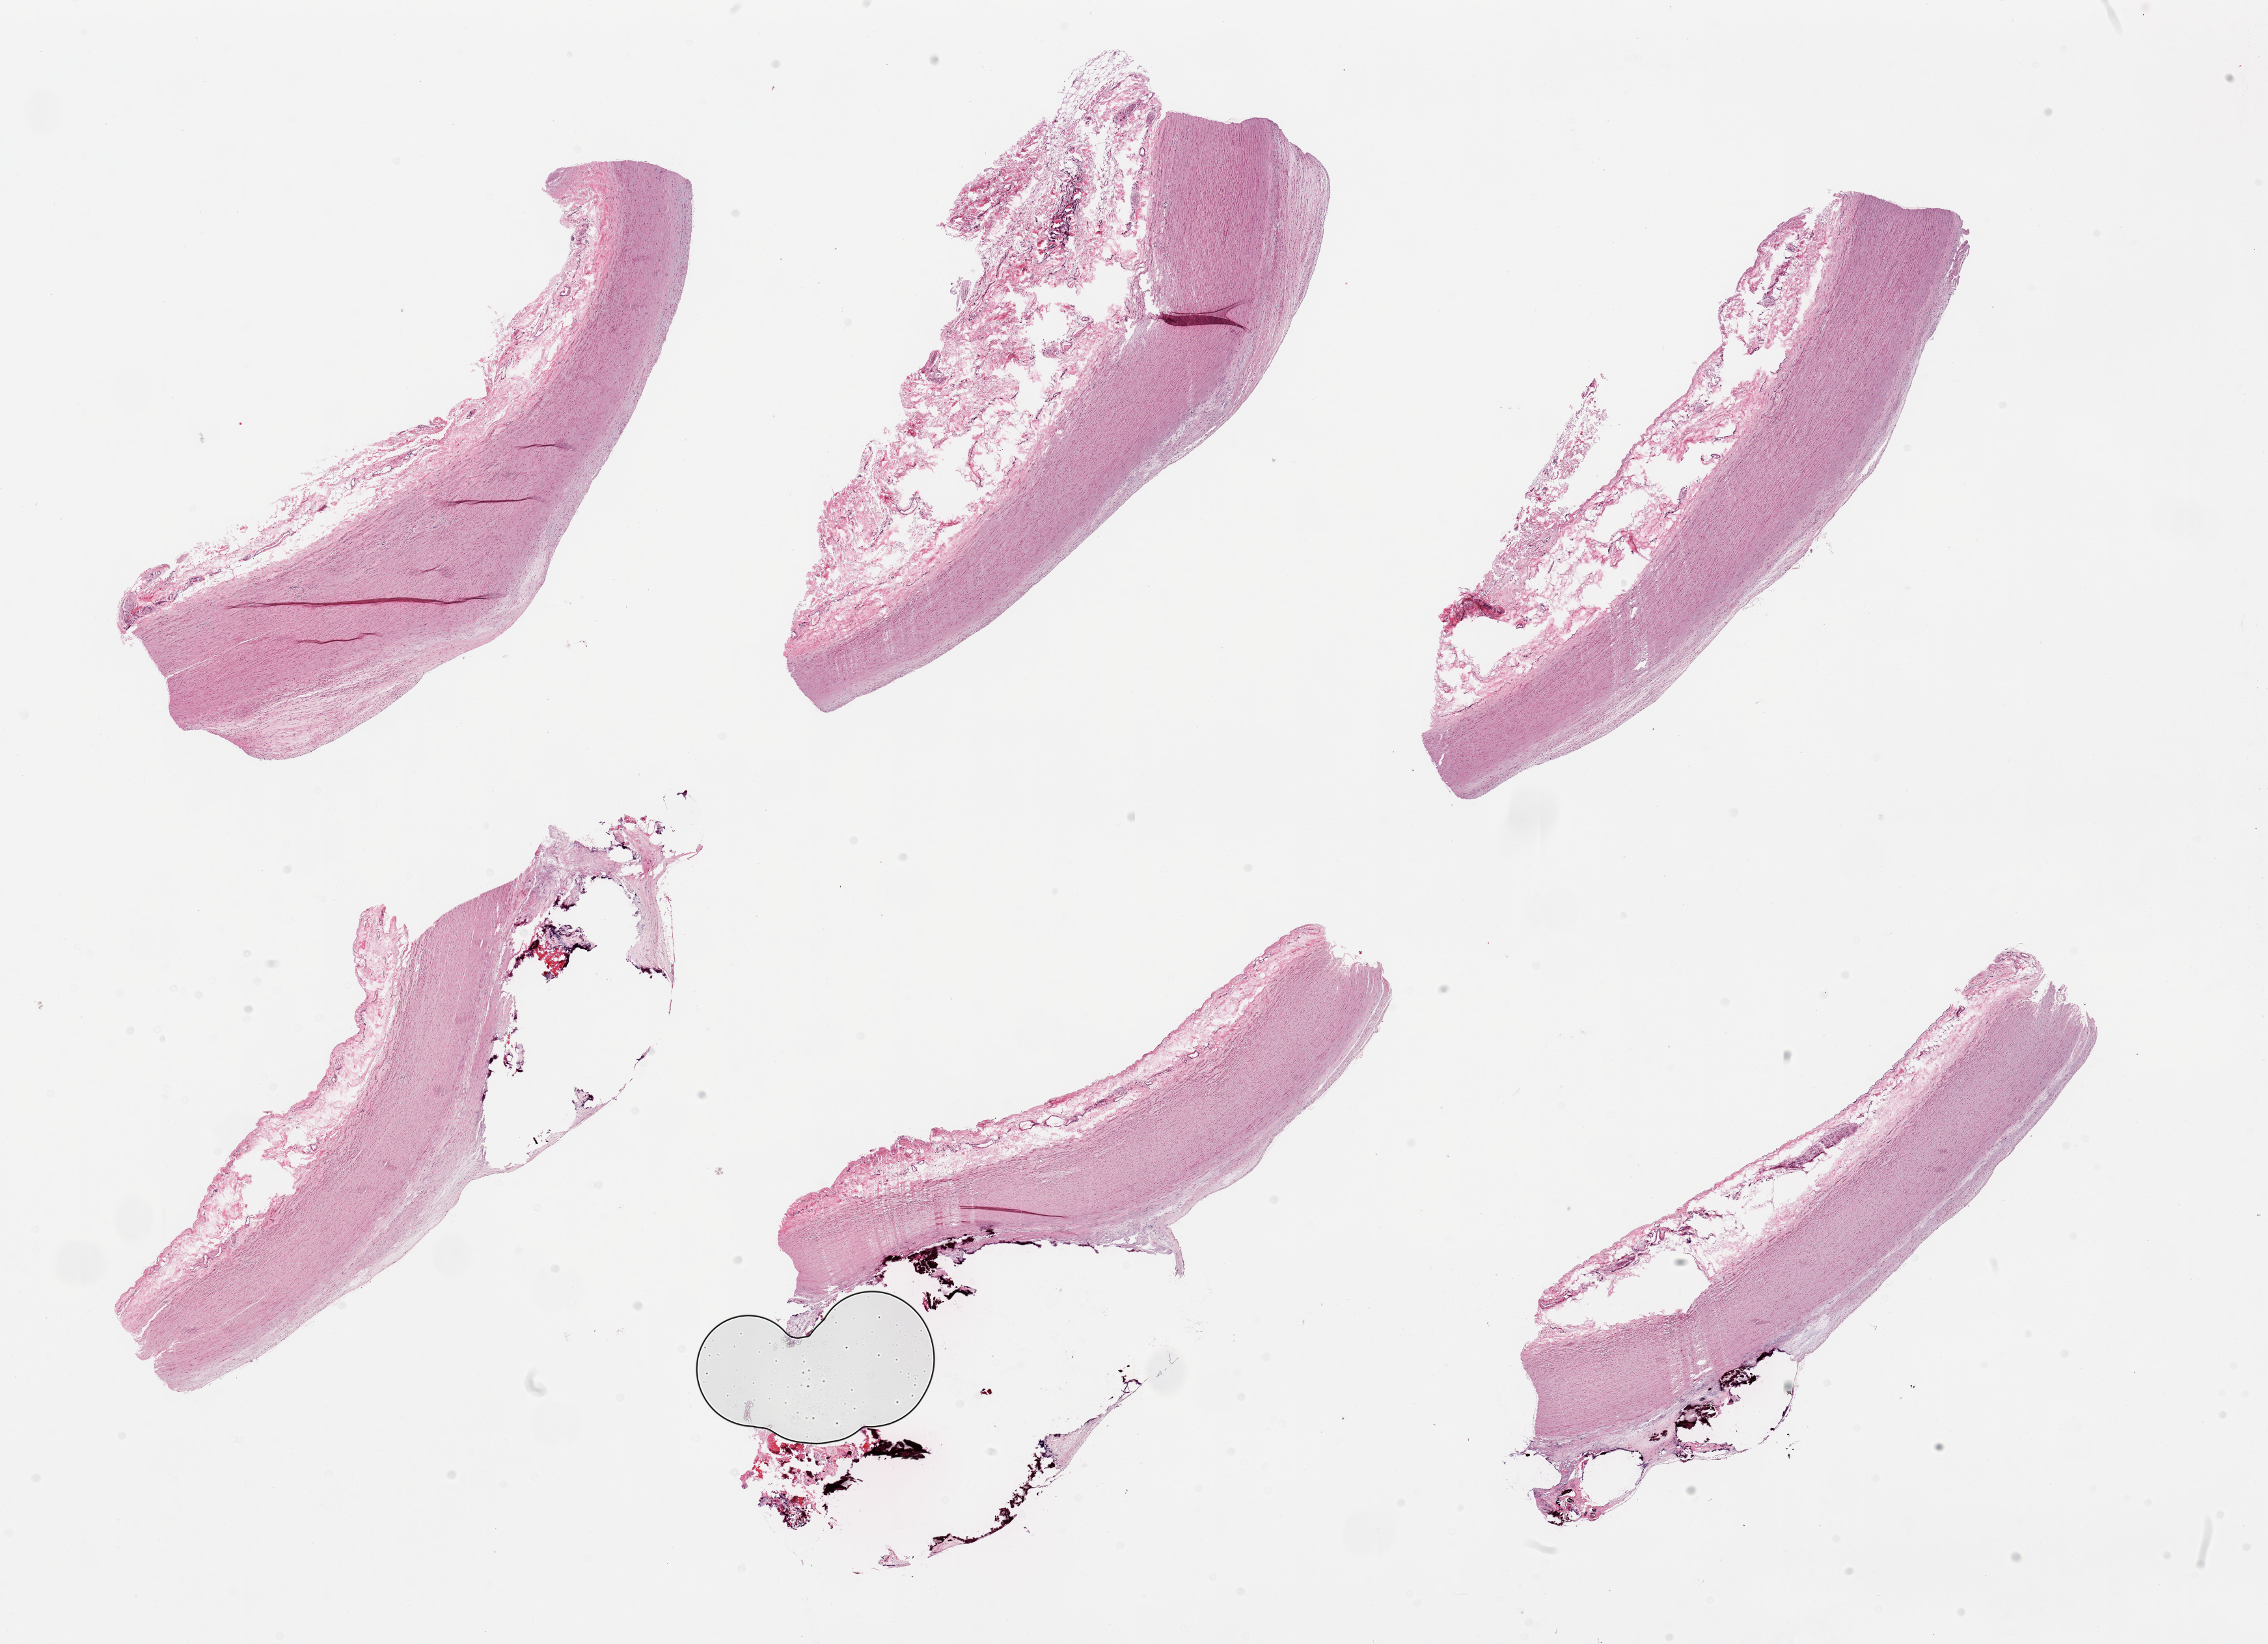
Hematoxylin and eosin (H&E) whole-slide image, shown as a low-resolution overview of the whole scanned area (about 27.6 x 20.0 mm, slide scanned at 20x). PAXgene-fixed paraffin-embedded (PFPE) section. Section of aorta (target tissue). Tissue donor sample. Female donor.
Pathologist's review note for this sample: 6 pieces; large calcified plaque in 3 of 6 pieces; flat plaques in other 3; untrimmed adventitia up to 1.7 mm thick.